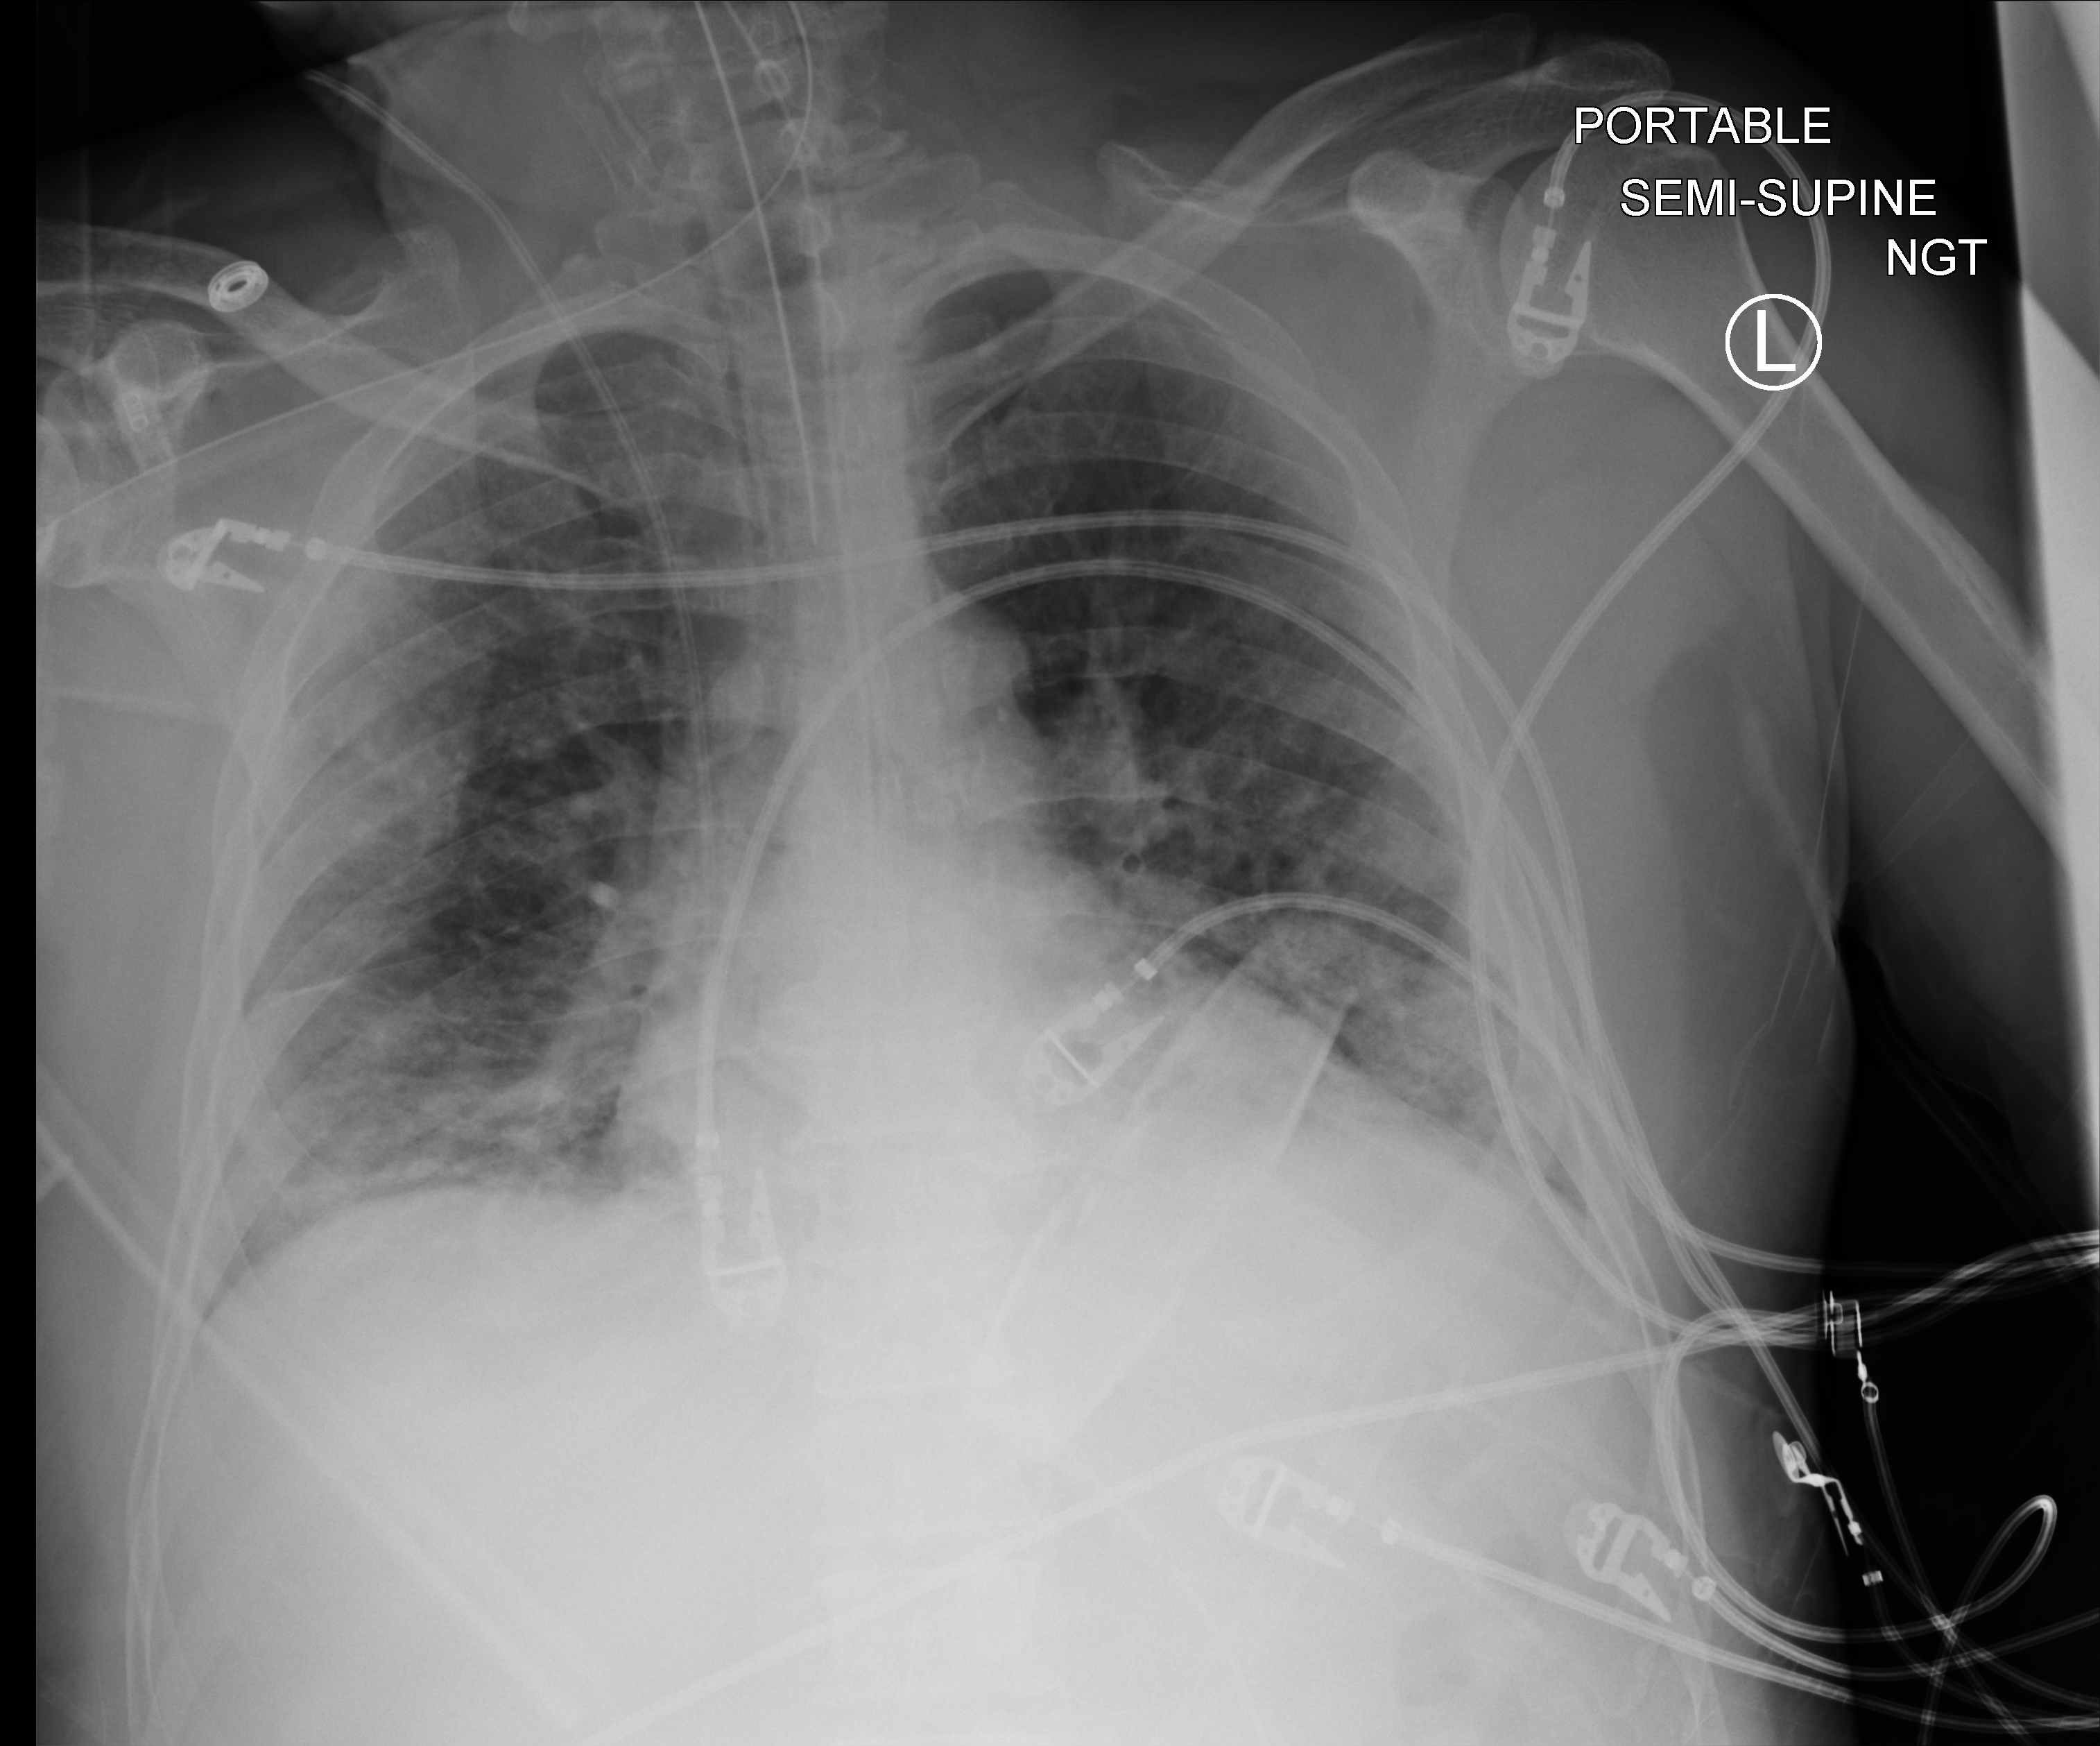
Chest X-ray (portable), anteroposterior (AP) projection. Patient hospitalised with COVID-19; male, aged 18–59 years.
From the hospital-stay record, not from the radiograph (when in the stay this image was taken is not recorded):
- mechanically ventilated during this hospital stay: yes